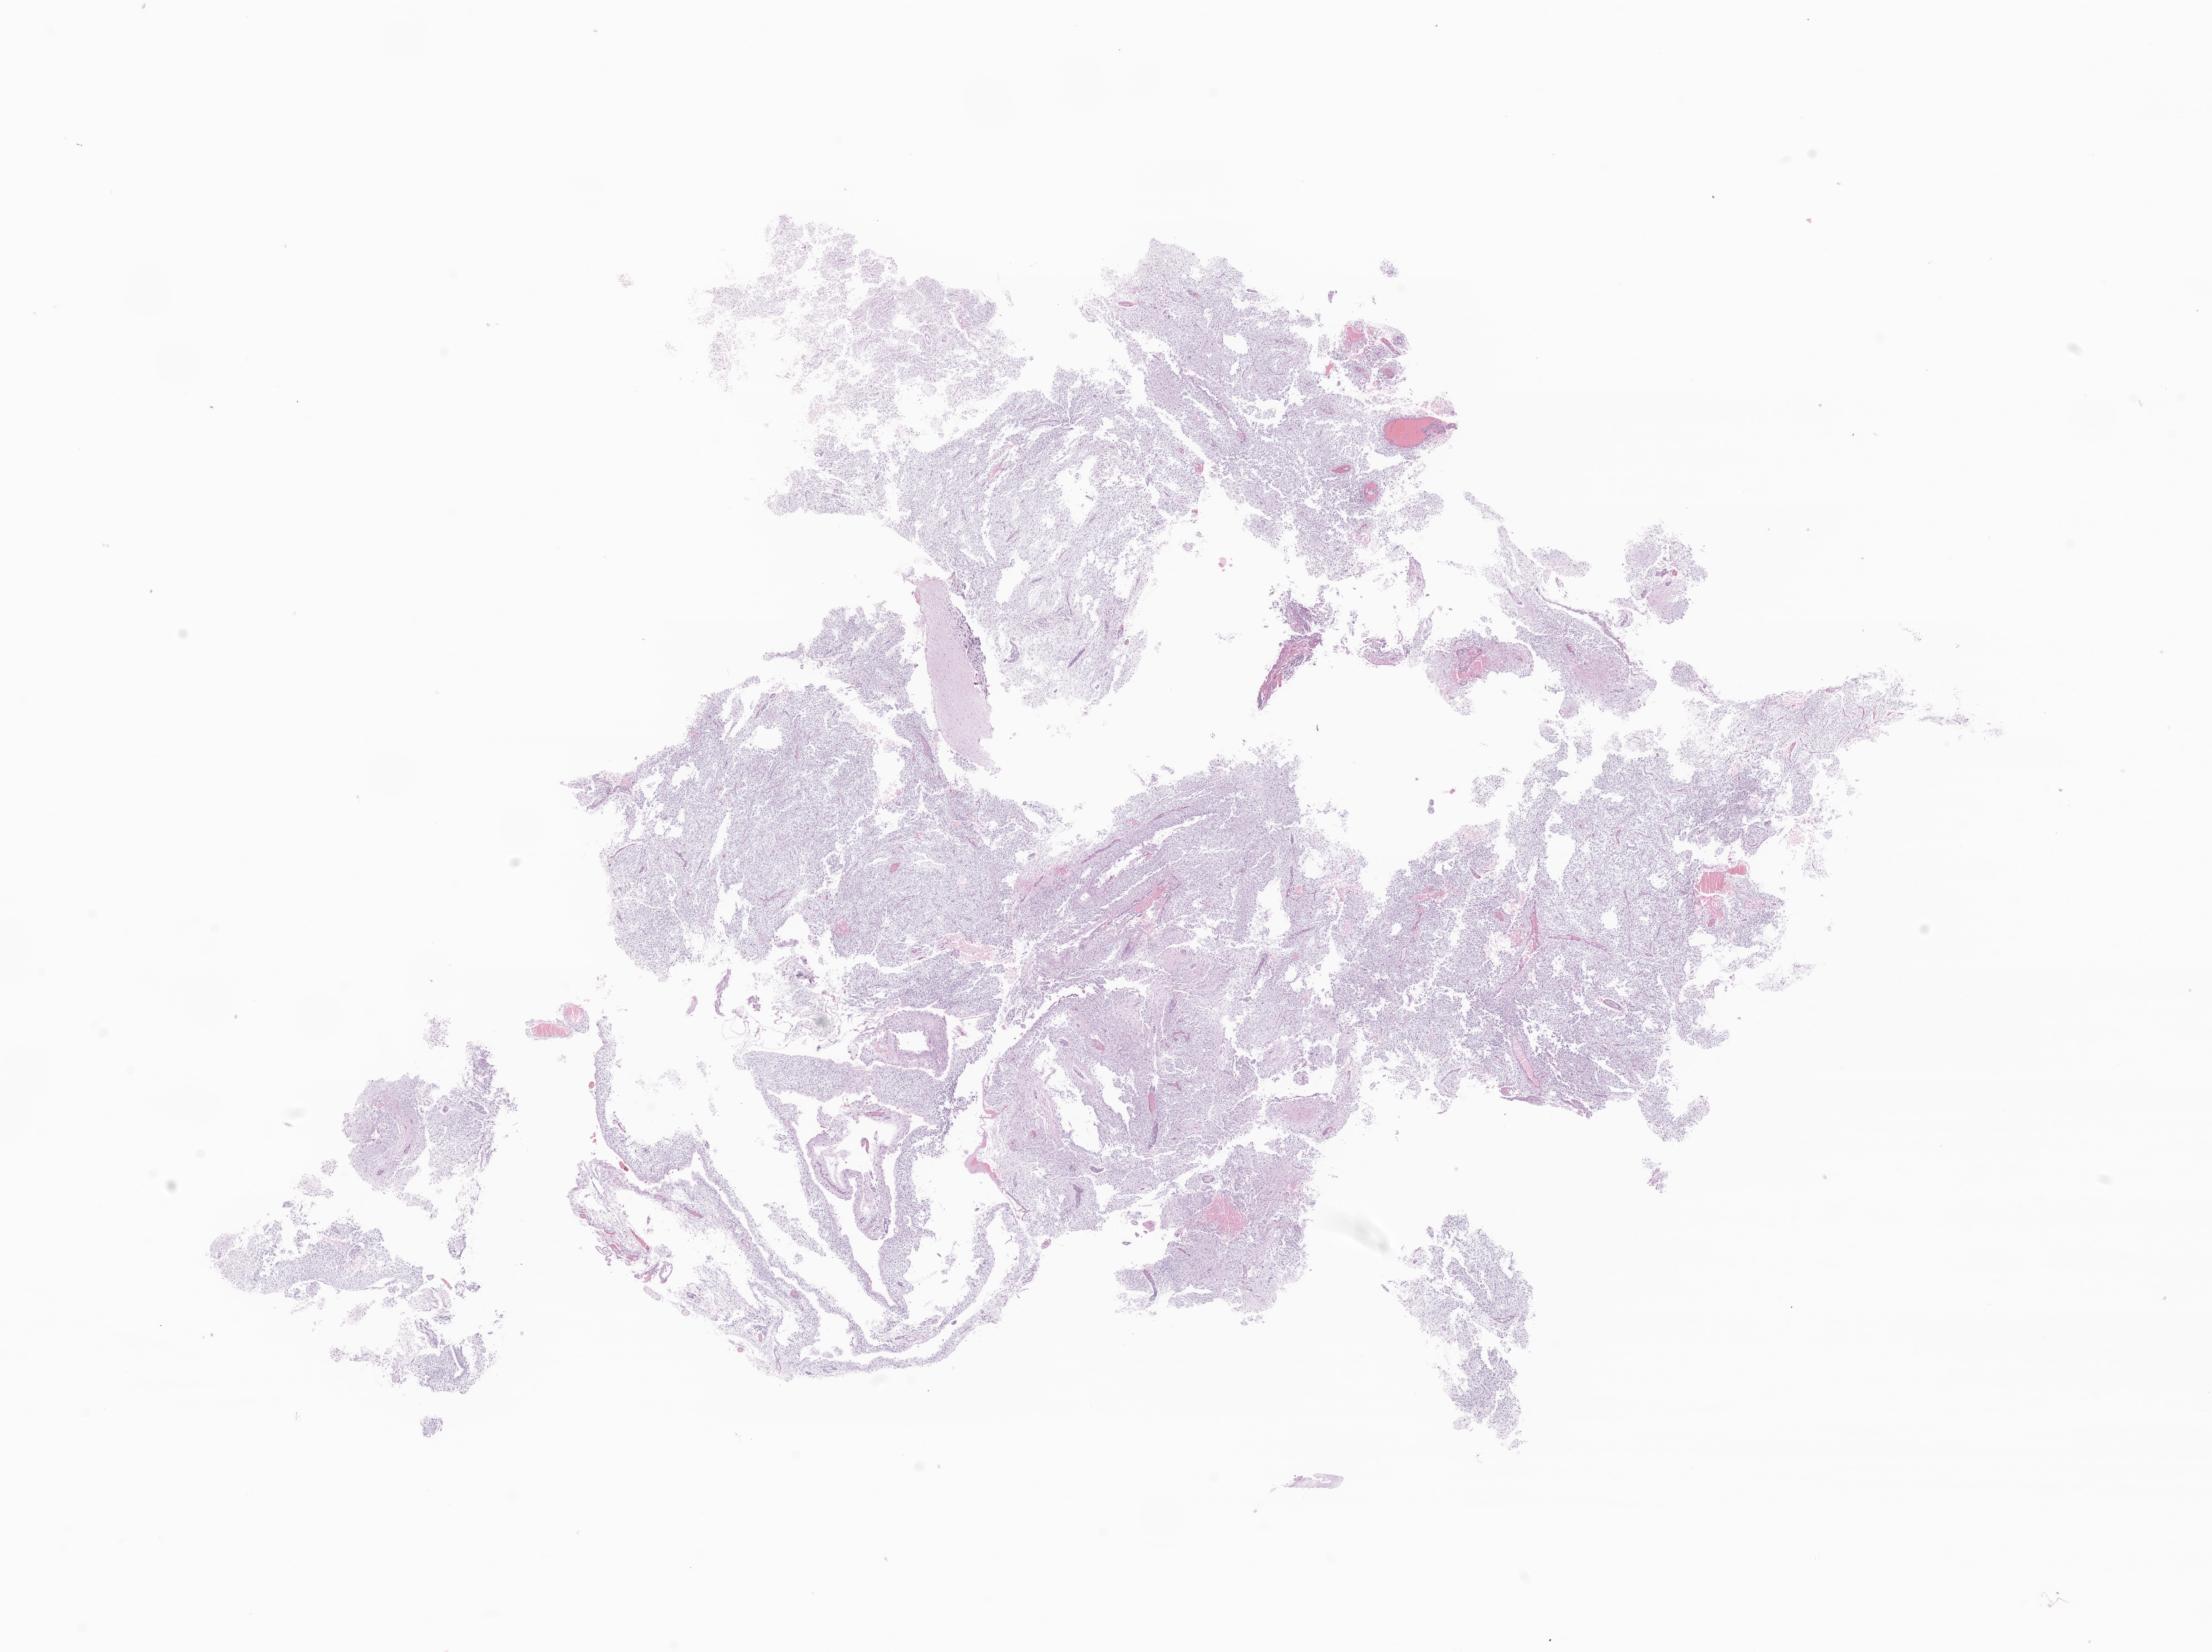
Digitized haematoxylin and eosin-stained section of tumor tissue from the brain — whole scanned area (about 20.5 x 15.3 mm) shown as a low-resolution overview; FFPE section. Patient: male, age 93 months.
Diagnosis: Pilocytic astrocytoma.